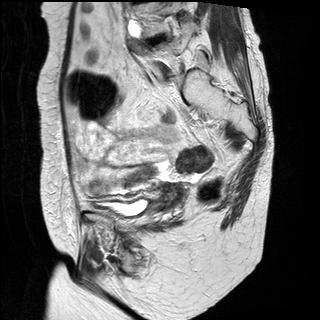
Pelvic MRI for cervical cancer, one sagittal slice; T2-weighted; 1.5 T; TE 89 ms, TR 3890 ms; 4 mm slice thickness; 320 × 320 image matrix, field of view 260 × 260 mm. Female patient, age 61 years.
Outlined on this slice (expert manual segmentation):
- uterus and cervix: box from (x=153, y=180) to (x=188, y=214) px